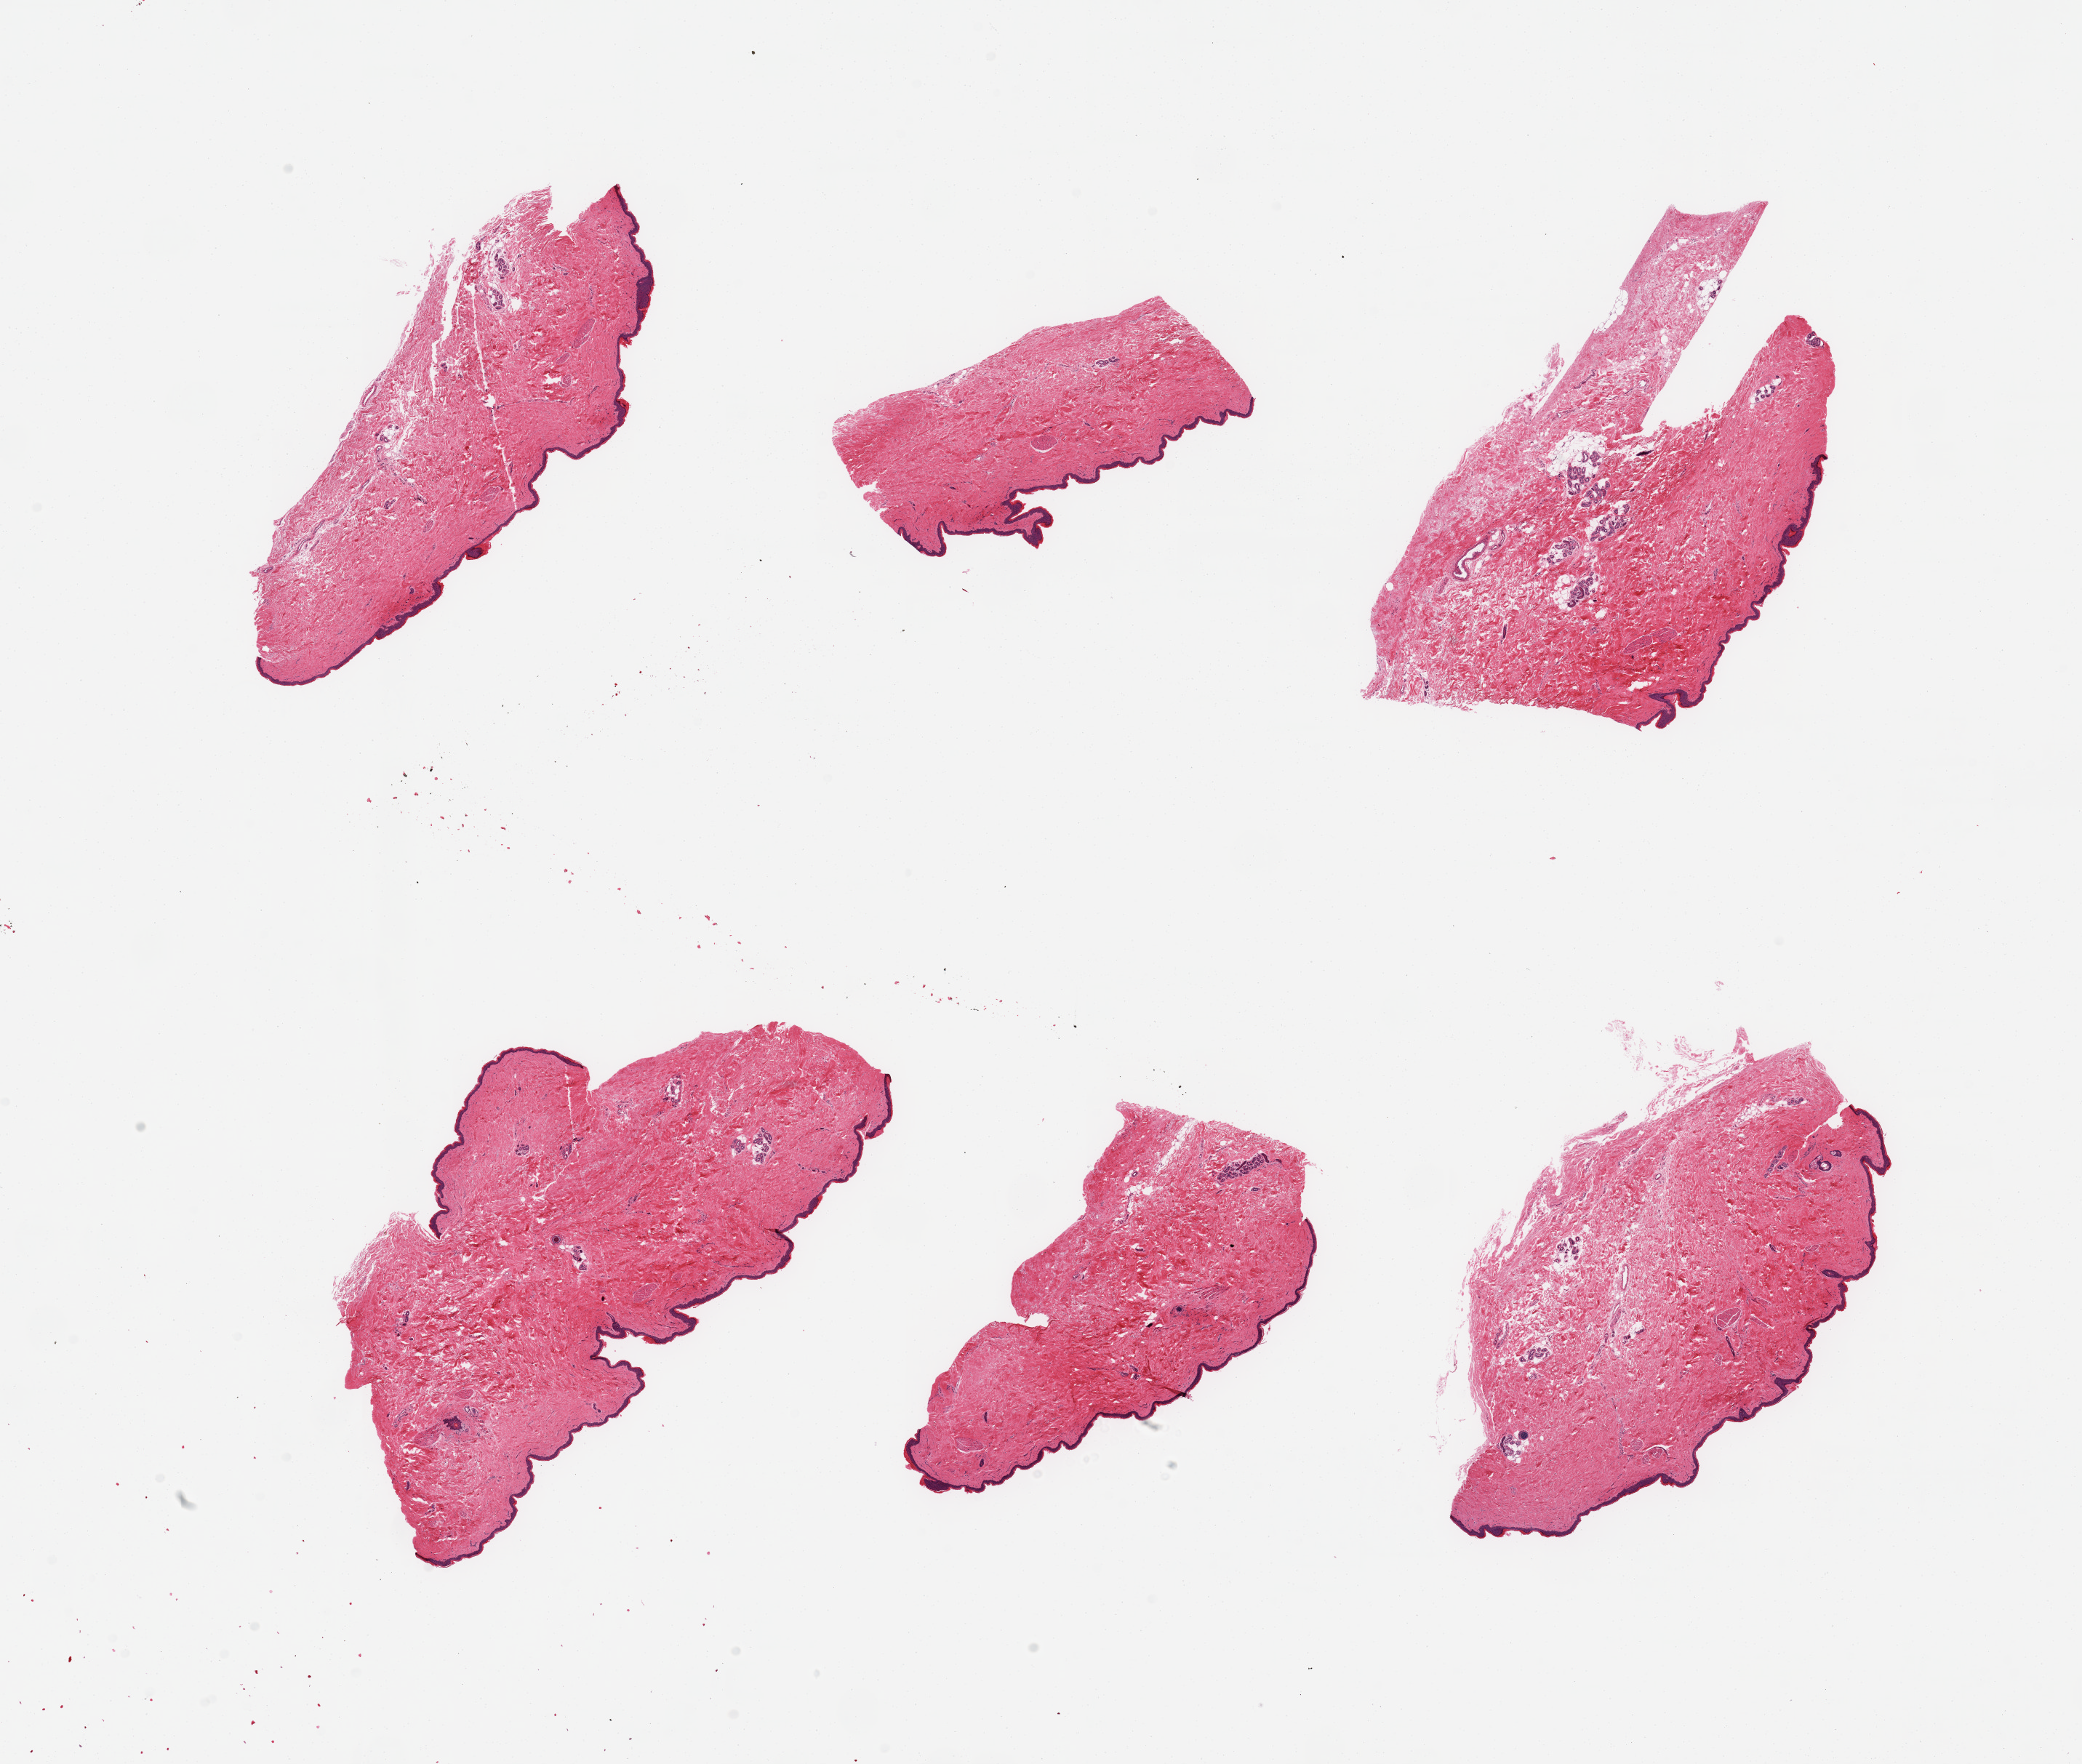
Hematoxylin and eosin (H&E) whole-slide image — low-resolution overview of the scanned area, about 22.6 x 19.2 mm. PAXgene-fixed paraffin-embedded (PFPE) section. Sampled site (target tissue): skin of suprapubic region. Tissue donor sample. Female donor.
- reviewer comment on this tissue sample: 6 pieces; small amounts of periadnexal fat